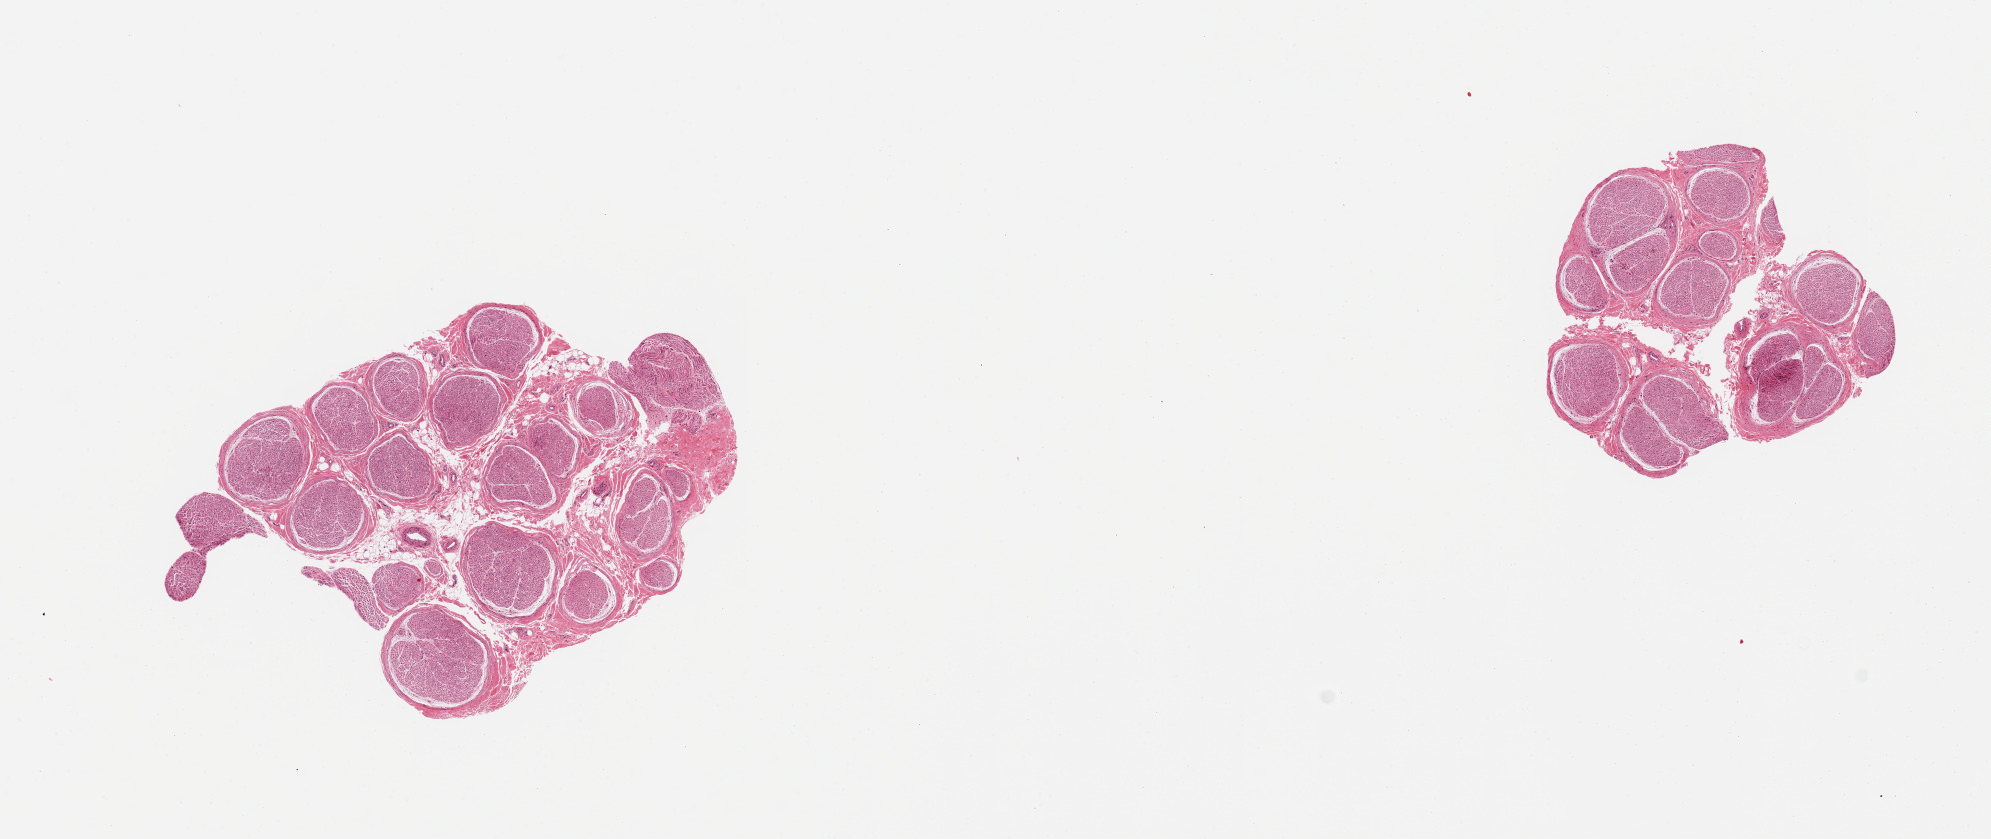
H&E whole-slide image, brightfield — low-resolution overview of the scanned area, about 15.8 x 6.6 mm; PAXgene-fixed paraffin-embedded (PFPE) section; sampled site (target tissue): tibial nerve; donor tissue sample. Donor: female.
Review note (as recorded): 2 pieces, clean specimen.